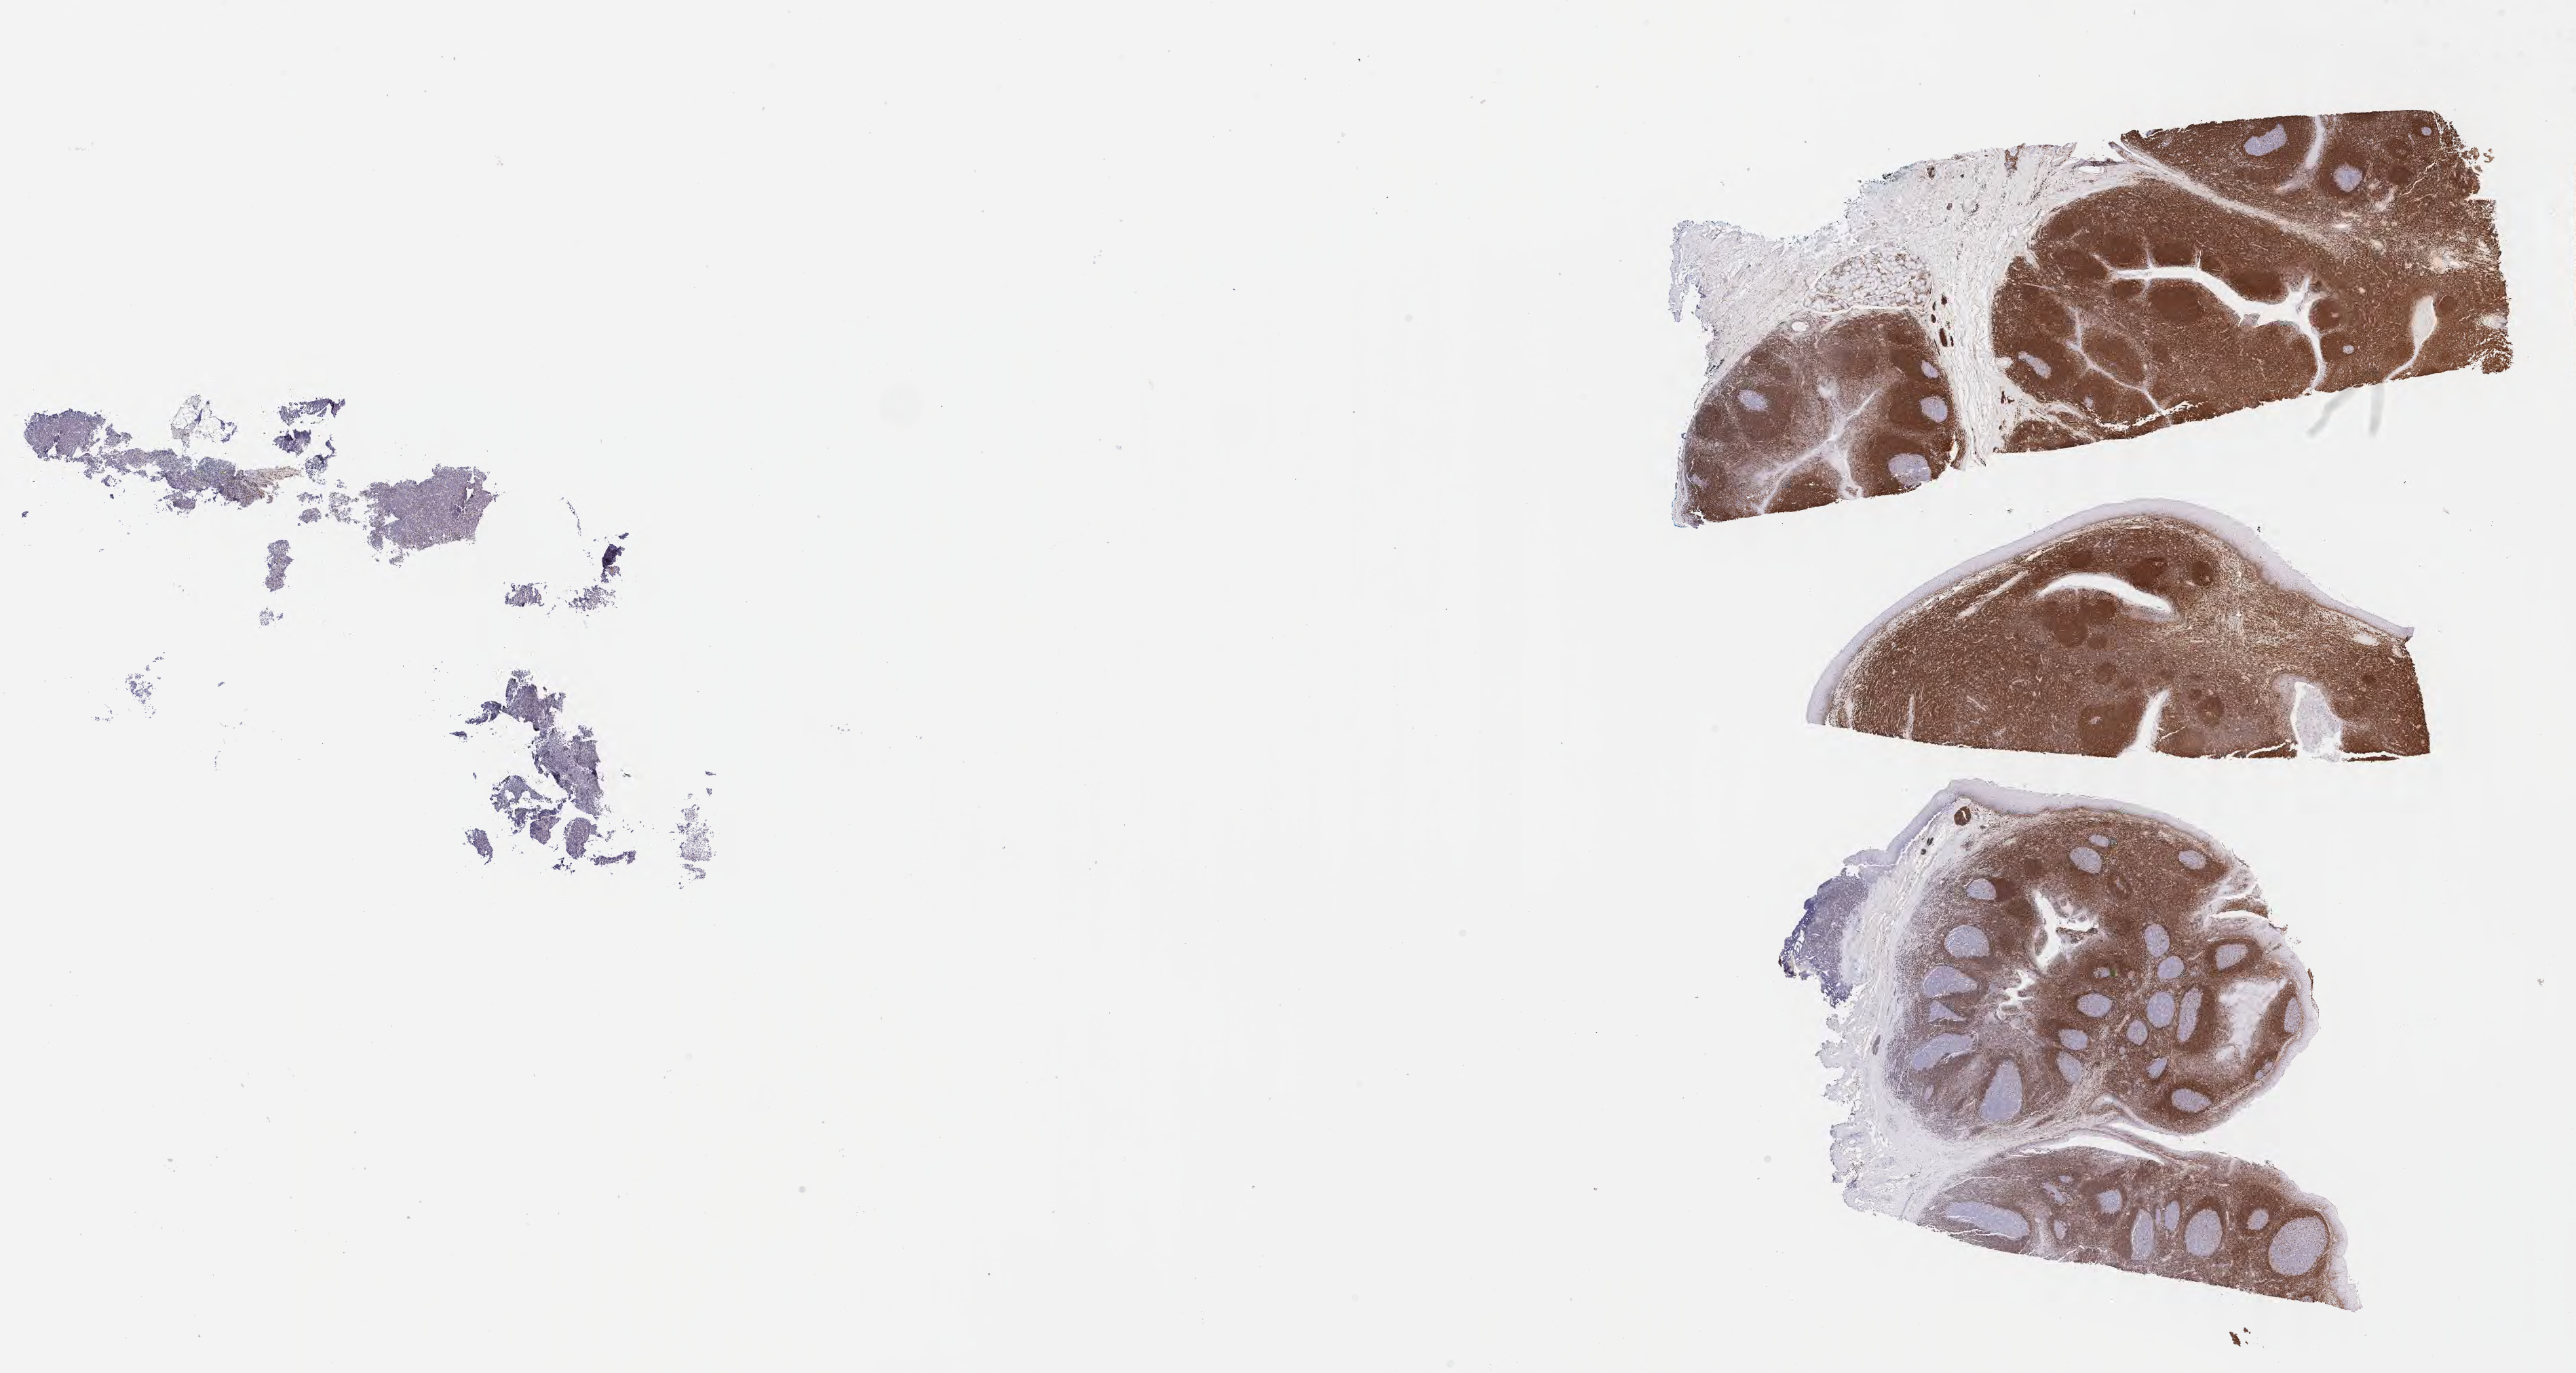
Whole-slide image, immunohistochemical stain for BCL2, low-resolution overview of the scanned area, about 30.7 x 16.4 mm, tumor tissue, anatomic site: cranium. Female, age 1 years at initial diagnosis.
Histologic diagnosis: Burkitt lymphoma, NOS.